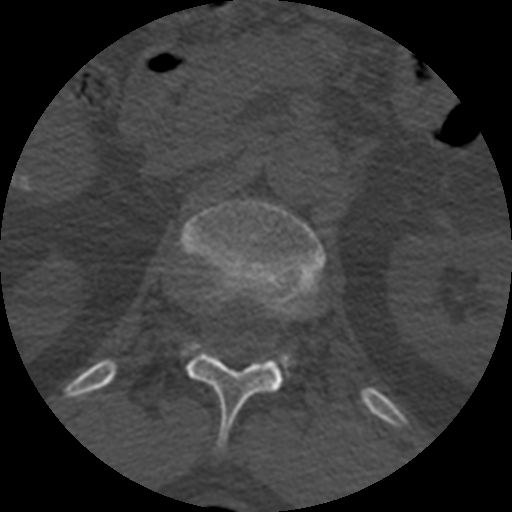
CT including the spine, one axial slice. Slice 376 of 399 in the series (ordered by position). Reconstruction kernel STANDARD. 120 kVp. Bone window (W 1800 / L 400 HU). 1.25 mm slice thickness. 512 × 512 image matrix, field of view 160 × 160 mm. Patient age 71 years. From the clinical record (not read from this slice): primary cancer: prostate.
Annotated regions visible in this slice (semi-automatic segmentation, software-assisted and operator-edited):
- L1 vertebra: box from (x=180, y=199) to (x=325, y=368) px
- T12 vertebra: (x=185, y=344)–(x=283, y=454)